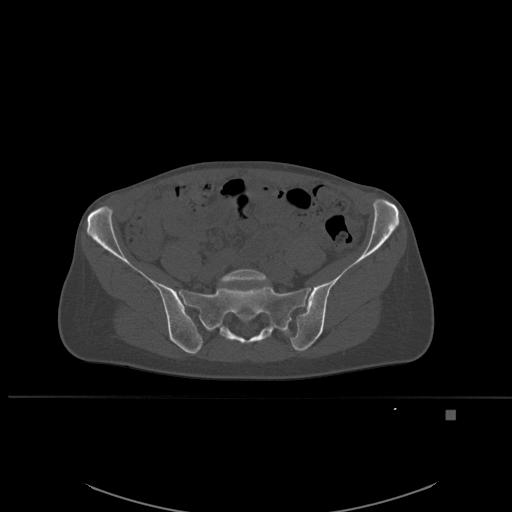
CT including the spine, one axial slice; slice 157 of 537 in the series (ordered by position); bone window (W 1800 / L 400 HU); 1.5 mm slice thickness; 512 × 512 image matrix, field of view 440 × 440 mm. Patient: female, 45 years. Case-level facts recorded for this patient, not image findings: primary cancer: lung.
Structures marked on this image (semi-automatically segmented with operator editing):
- L5 vertebra: bounding box <219,269,269,286> (left, top, right, bottom; pixels)